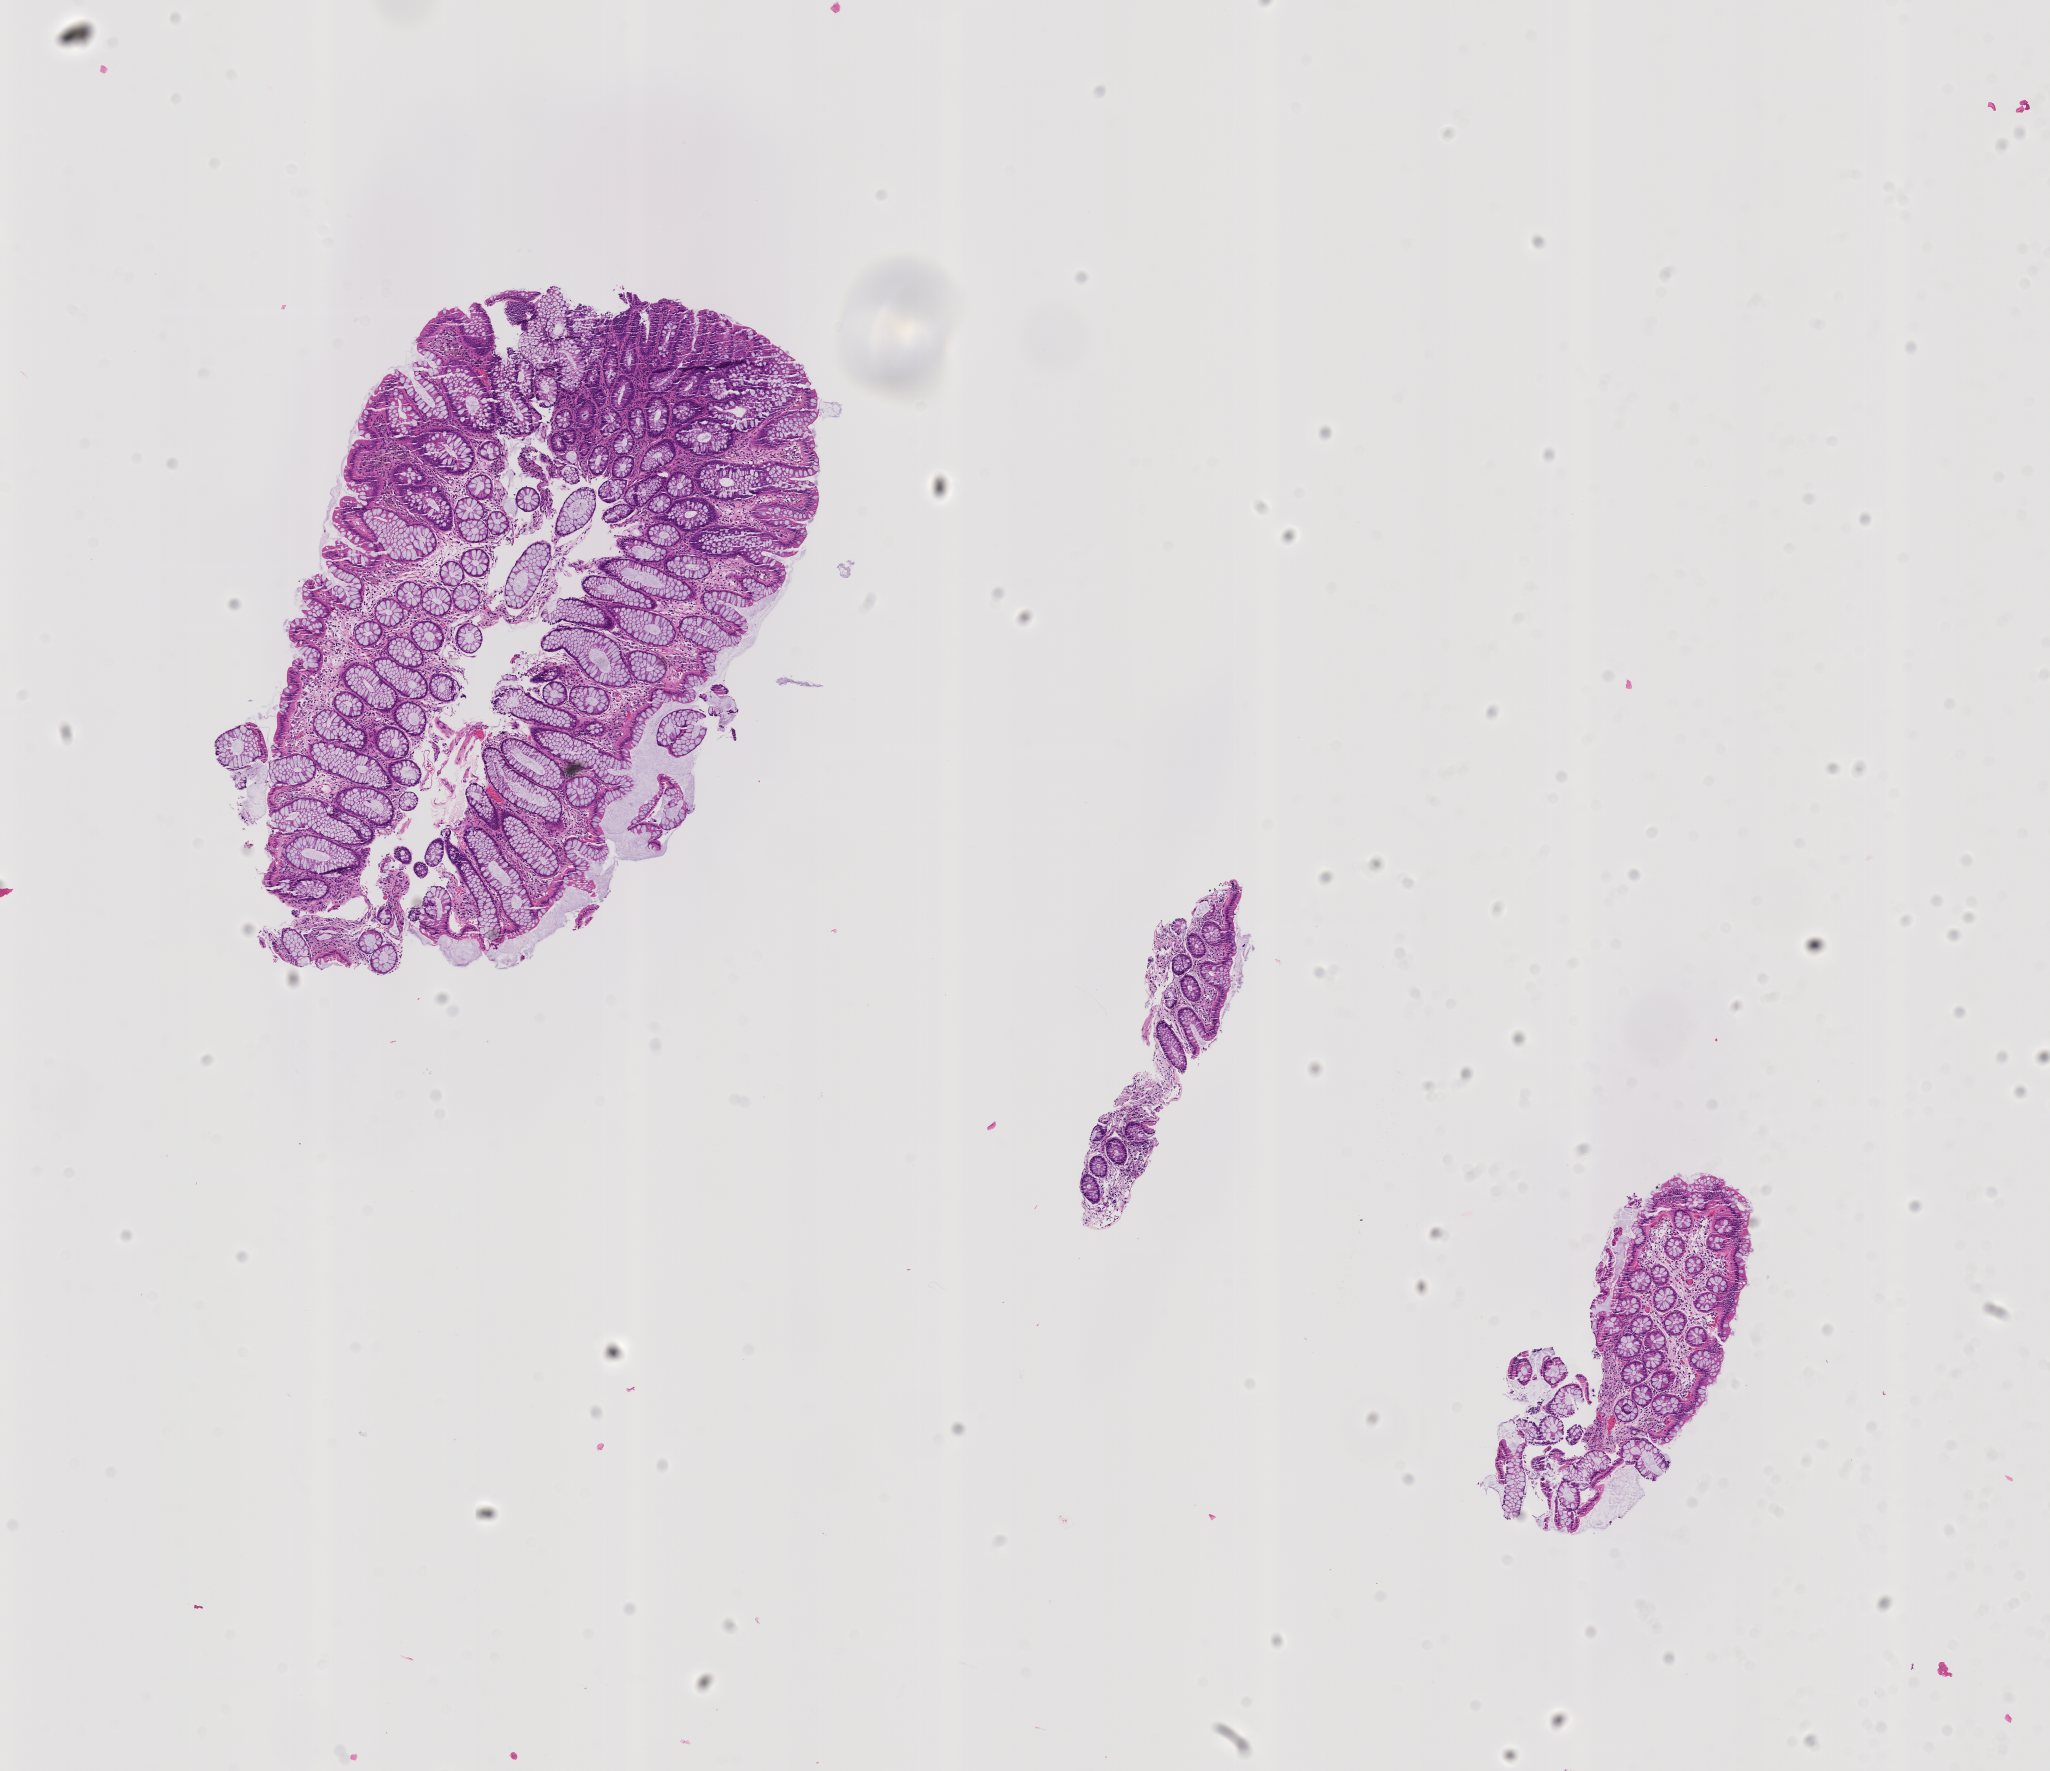
Hematoxylin and eosin (H&E) whole-slide image of a colon biopsy, shown as a low-resolution overview of the whole scanned area (about 8.2 x 7.1 mm); formalin-fixed, paraffin-embedded (FFPE) tissue; site: ascending colon. Patient: male.
- lesion category (as recorded): premalignant